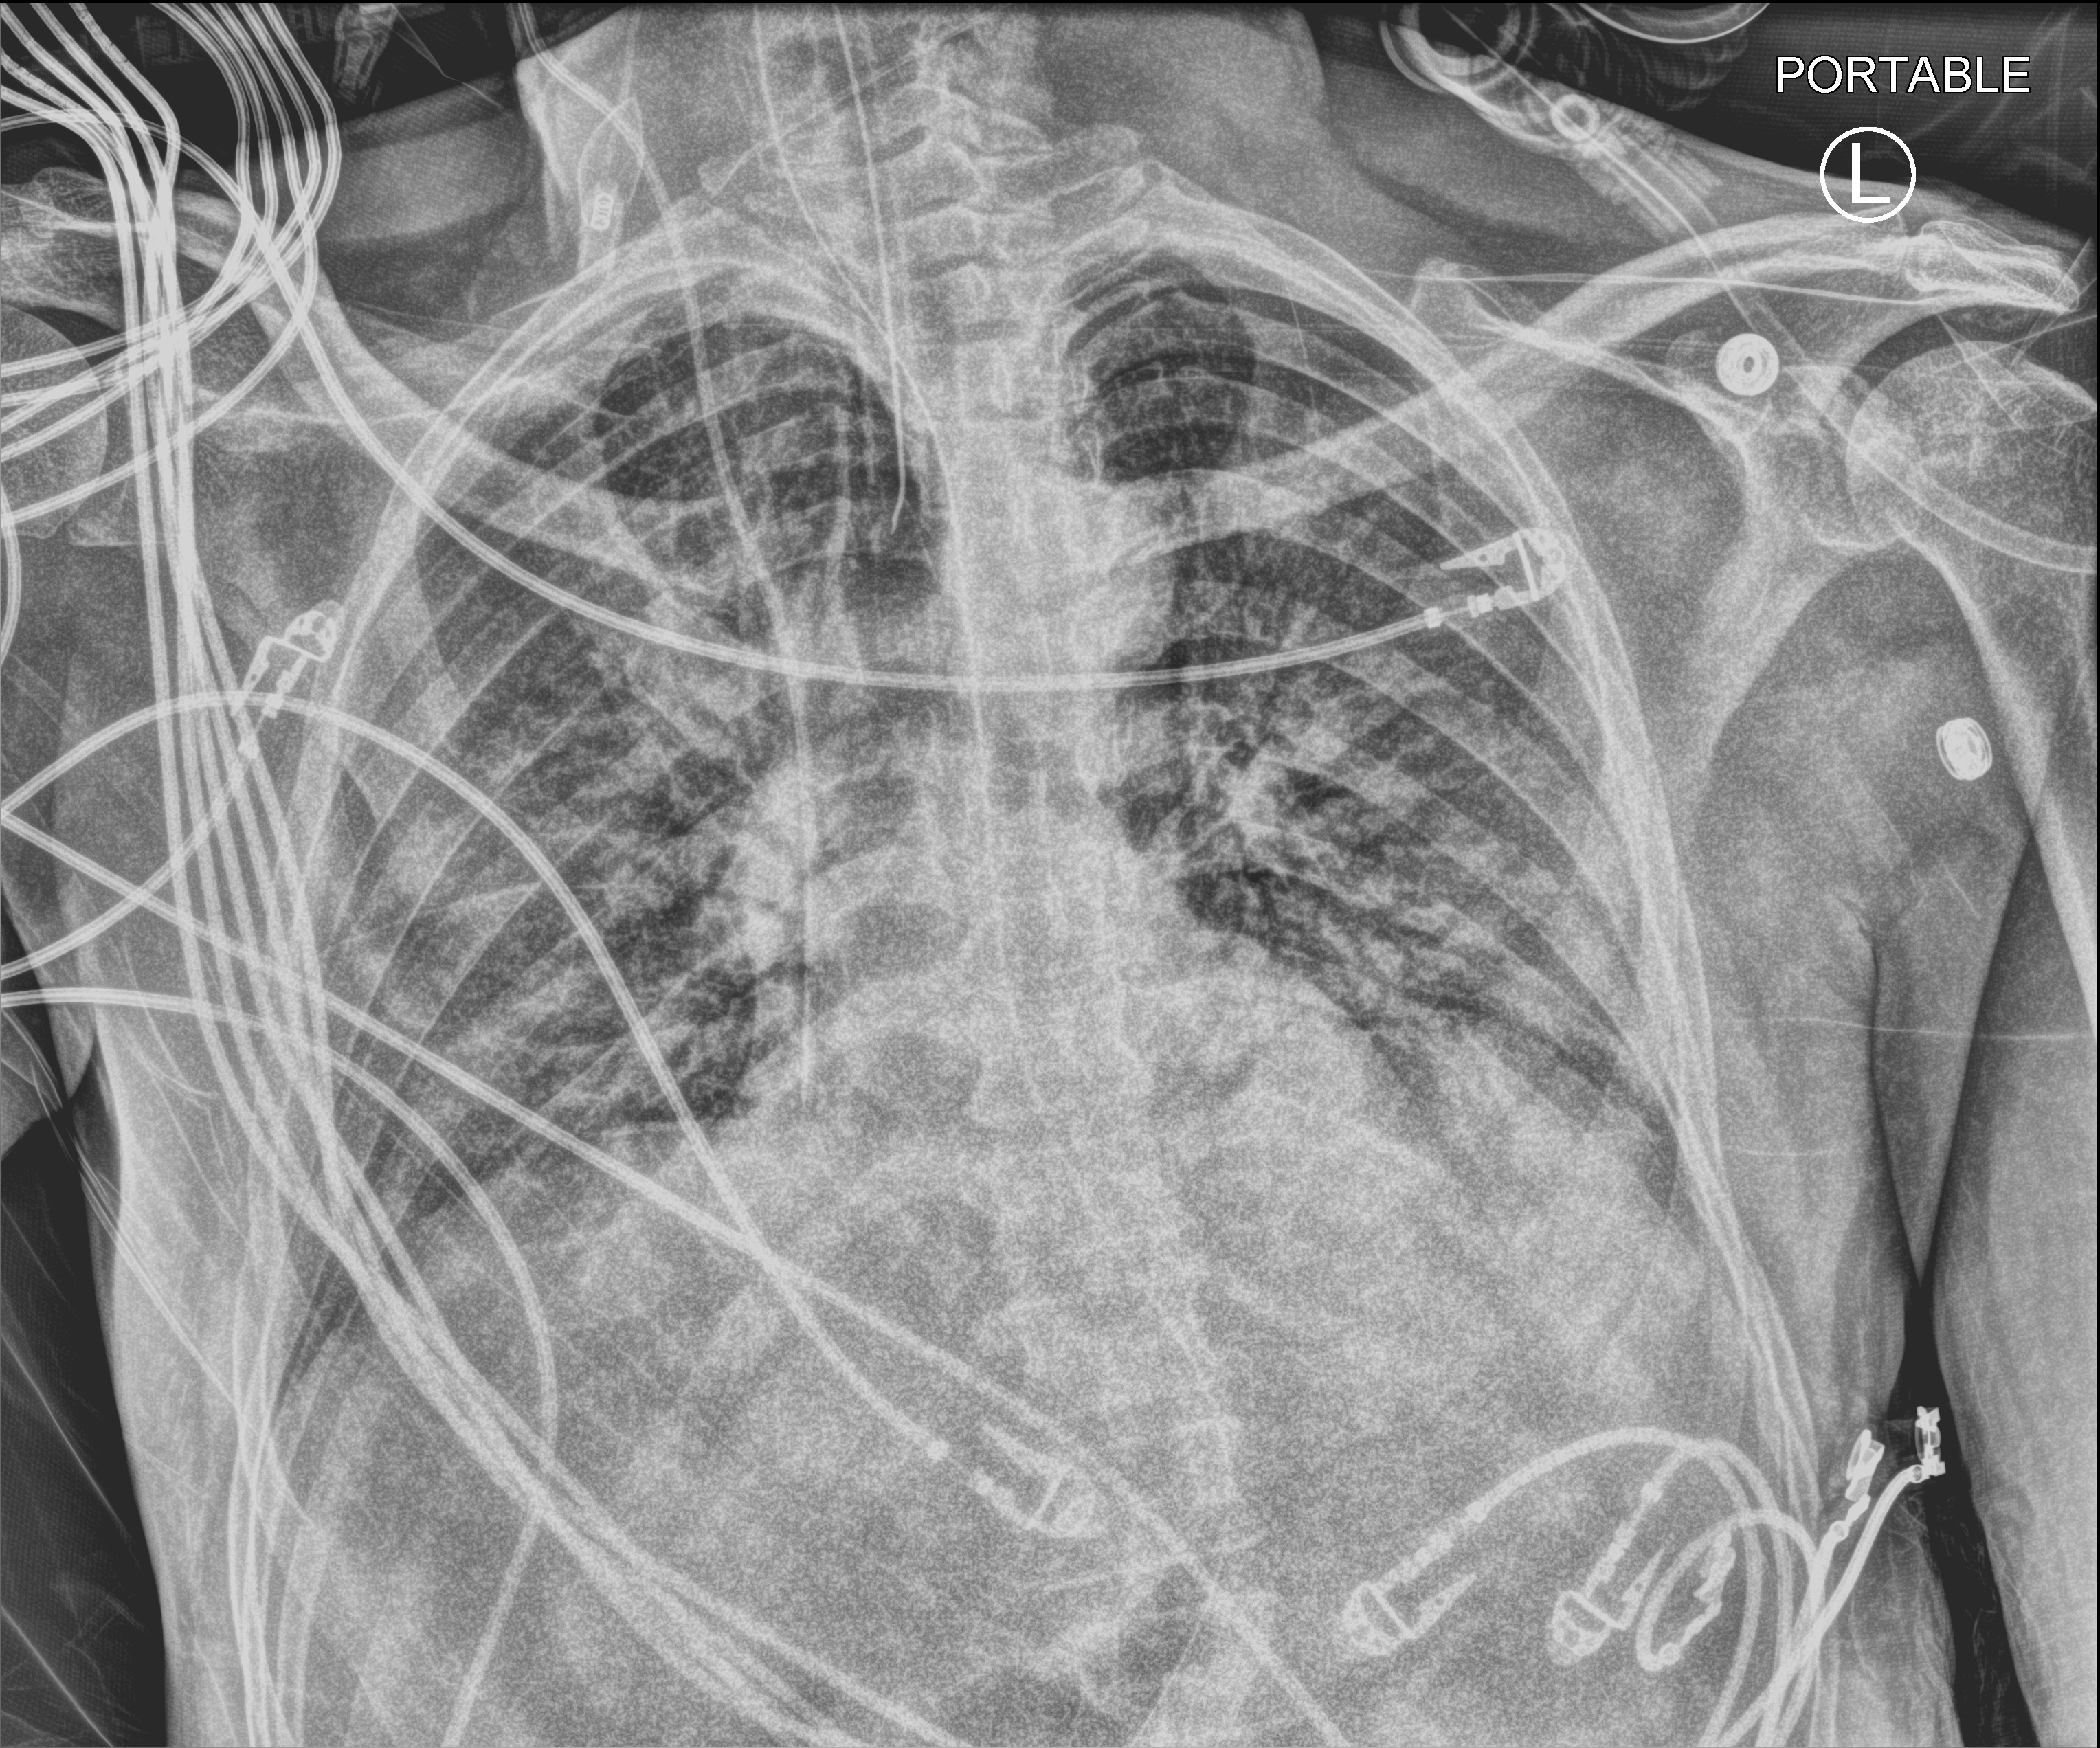
Chest X-ray (portable), anteroposterior (AP) projection. Patient hospitalised with COVID-19; male, aged 18–59 years.
Admission-level facts for this patient (not findings on this image; timing relative to this image not recorded): mechanically ventilated during this hospital stay: yes; admitted to intensive care during this hospital stay: yes.